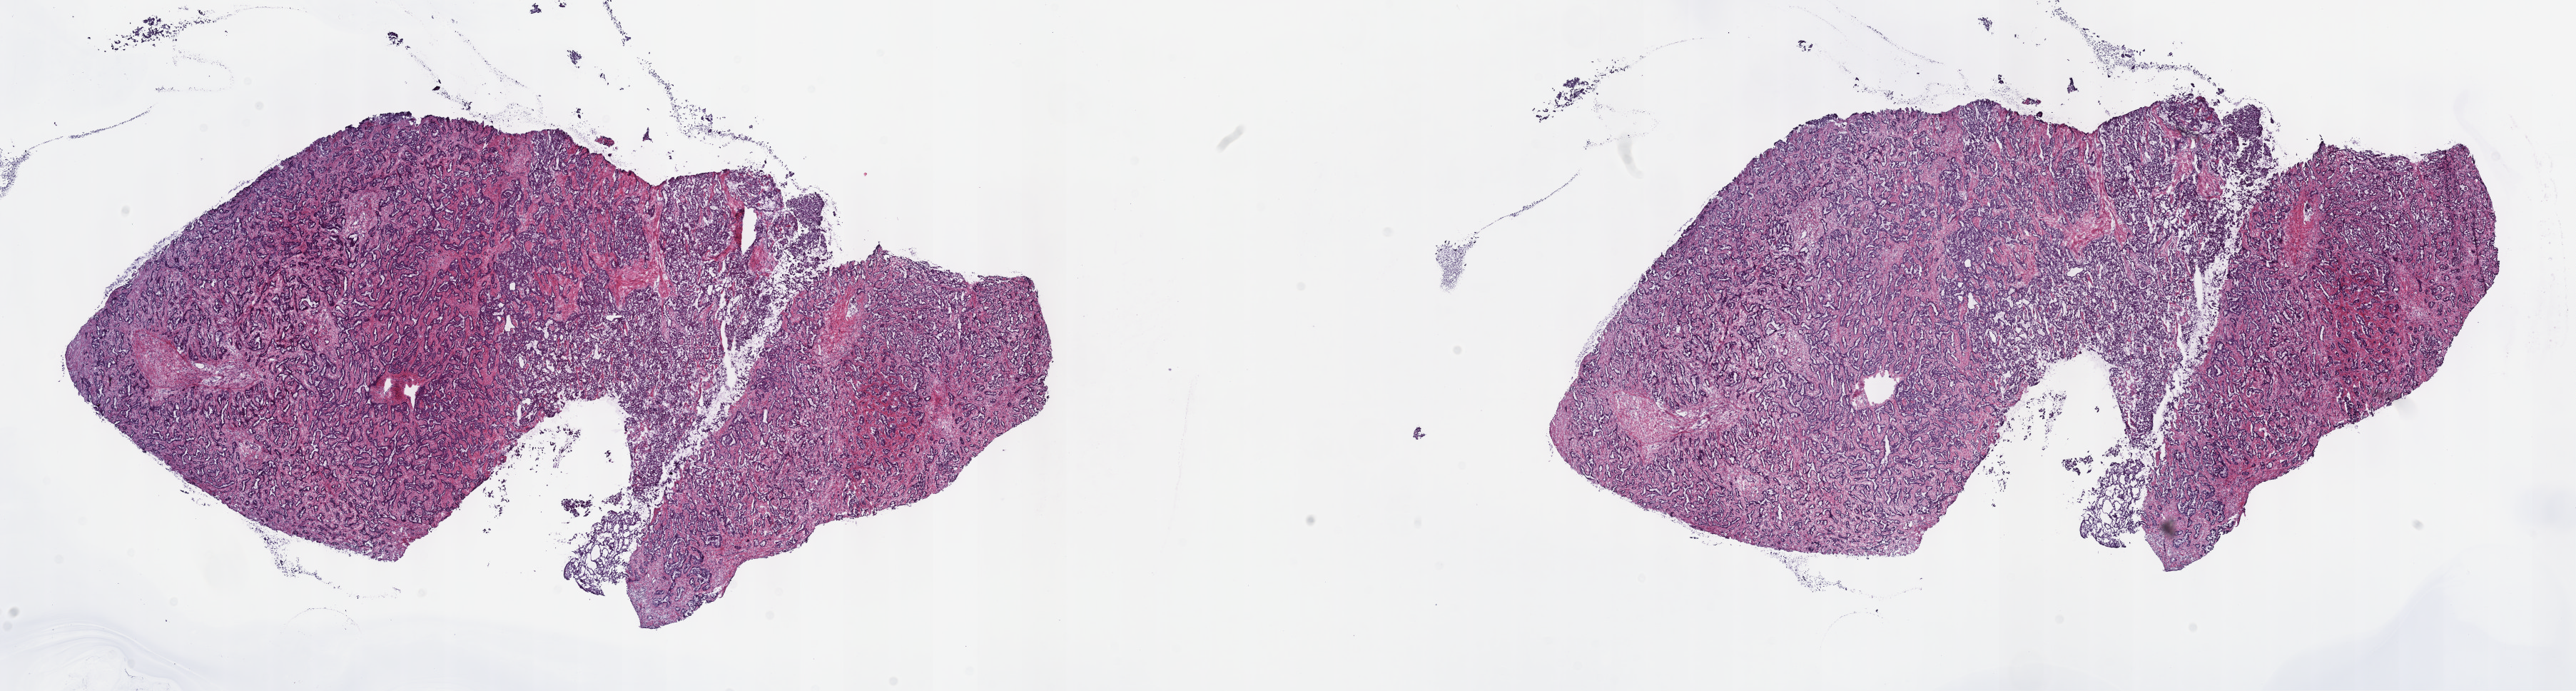
Hematoxylin and eosin (H&E) stained whole-slide image, whole scanned area (about 29.2 x 7.8 mm) shown as a low-resolution overview; frozen section from the top of the tissue portion; sample: primary tumour, bile duct. Female patient; age at initial diagnosis 59 years. Histologic grade: G2 (moderately differentiated). Composition of this section per pathologist review: tumour cells 100%, tumour nuclei 70%, normal cells 0%, stromal cells 0%, necrosis 0%. Inflammatory infiltration, as recorded: lymphocyte infiltration 2%, monocyte infiltration 0%, neutrophil infiltration 0%.
AJCC pathologic stage: I (7th edition). TNM: T1 NX M0. Histologic diagnosis: Cholangiocarcinoma (intrahepatic bile duct).